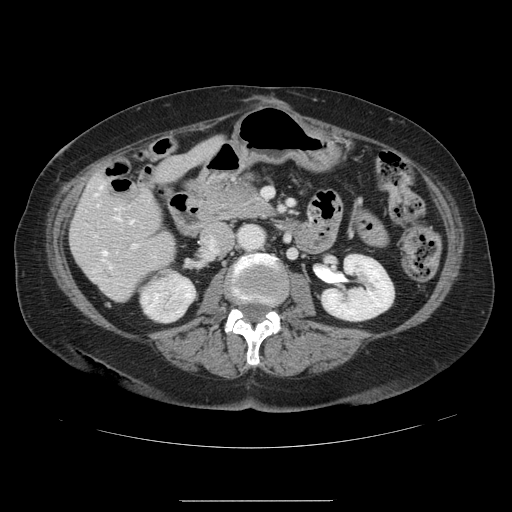
Contrast-enhanced abdominal CT, one axial slice. Slice 44 of 141 in the series (ordered by position). 120 kVp. Intravenous contrast given. Soft-tissue window (W 400 / L 40 HU). 2.5 mm slice thickness. 512 × 512 image matrix. Female patient, age 74 years. Case-level facts recorded for this patient, not image findings: diagnosis: colorectal cancer liver metastases, imaged before liver resection; multiple liver metastases: yes; largest metastasis: 7 cm; disease in both lobes: yes.
Outlined on this slice (outlined manually by an expert reader):
- hepatic veins: bounding box <95,186,132,267> (left, top, right, bottom; pixels)
- liver: <71,138,221,300>
- planned liver remnant (the part of the liver to remain after resection): <71,138,221,289>
- portal vein (with intrahepatic branches): <115,207,136,248>